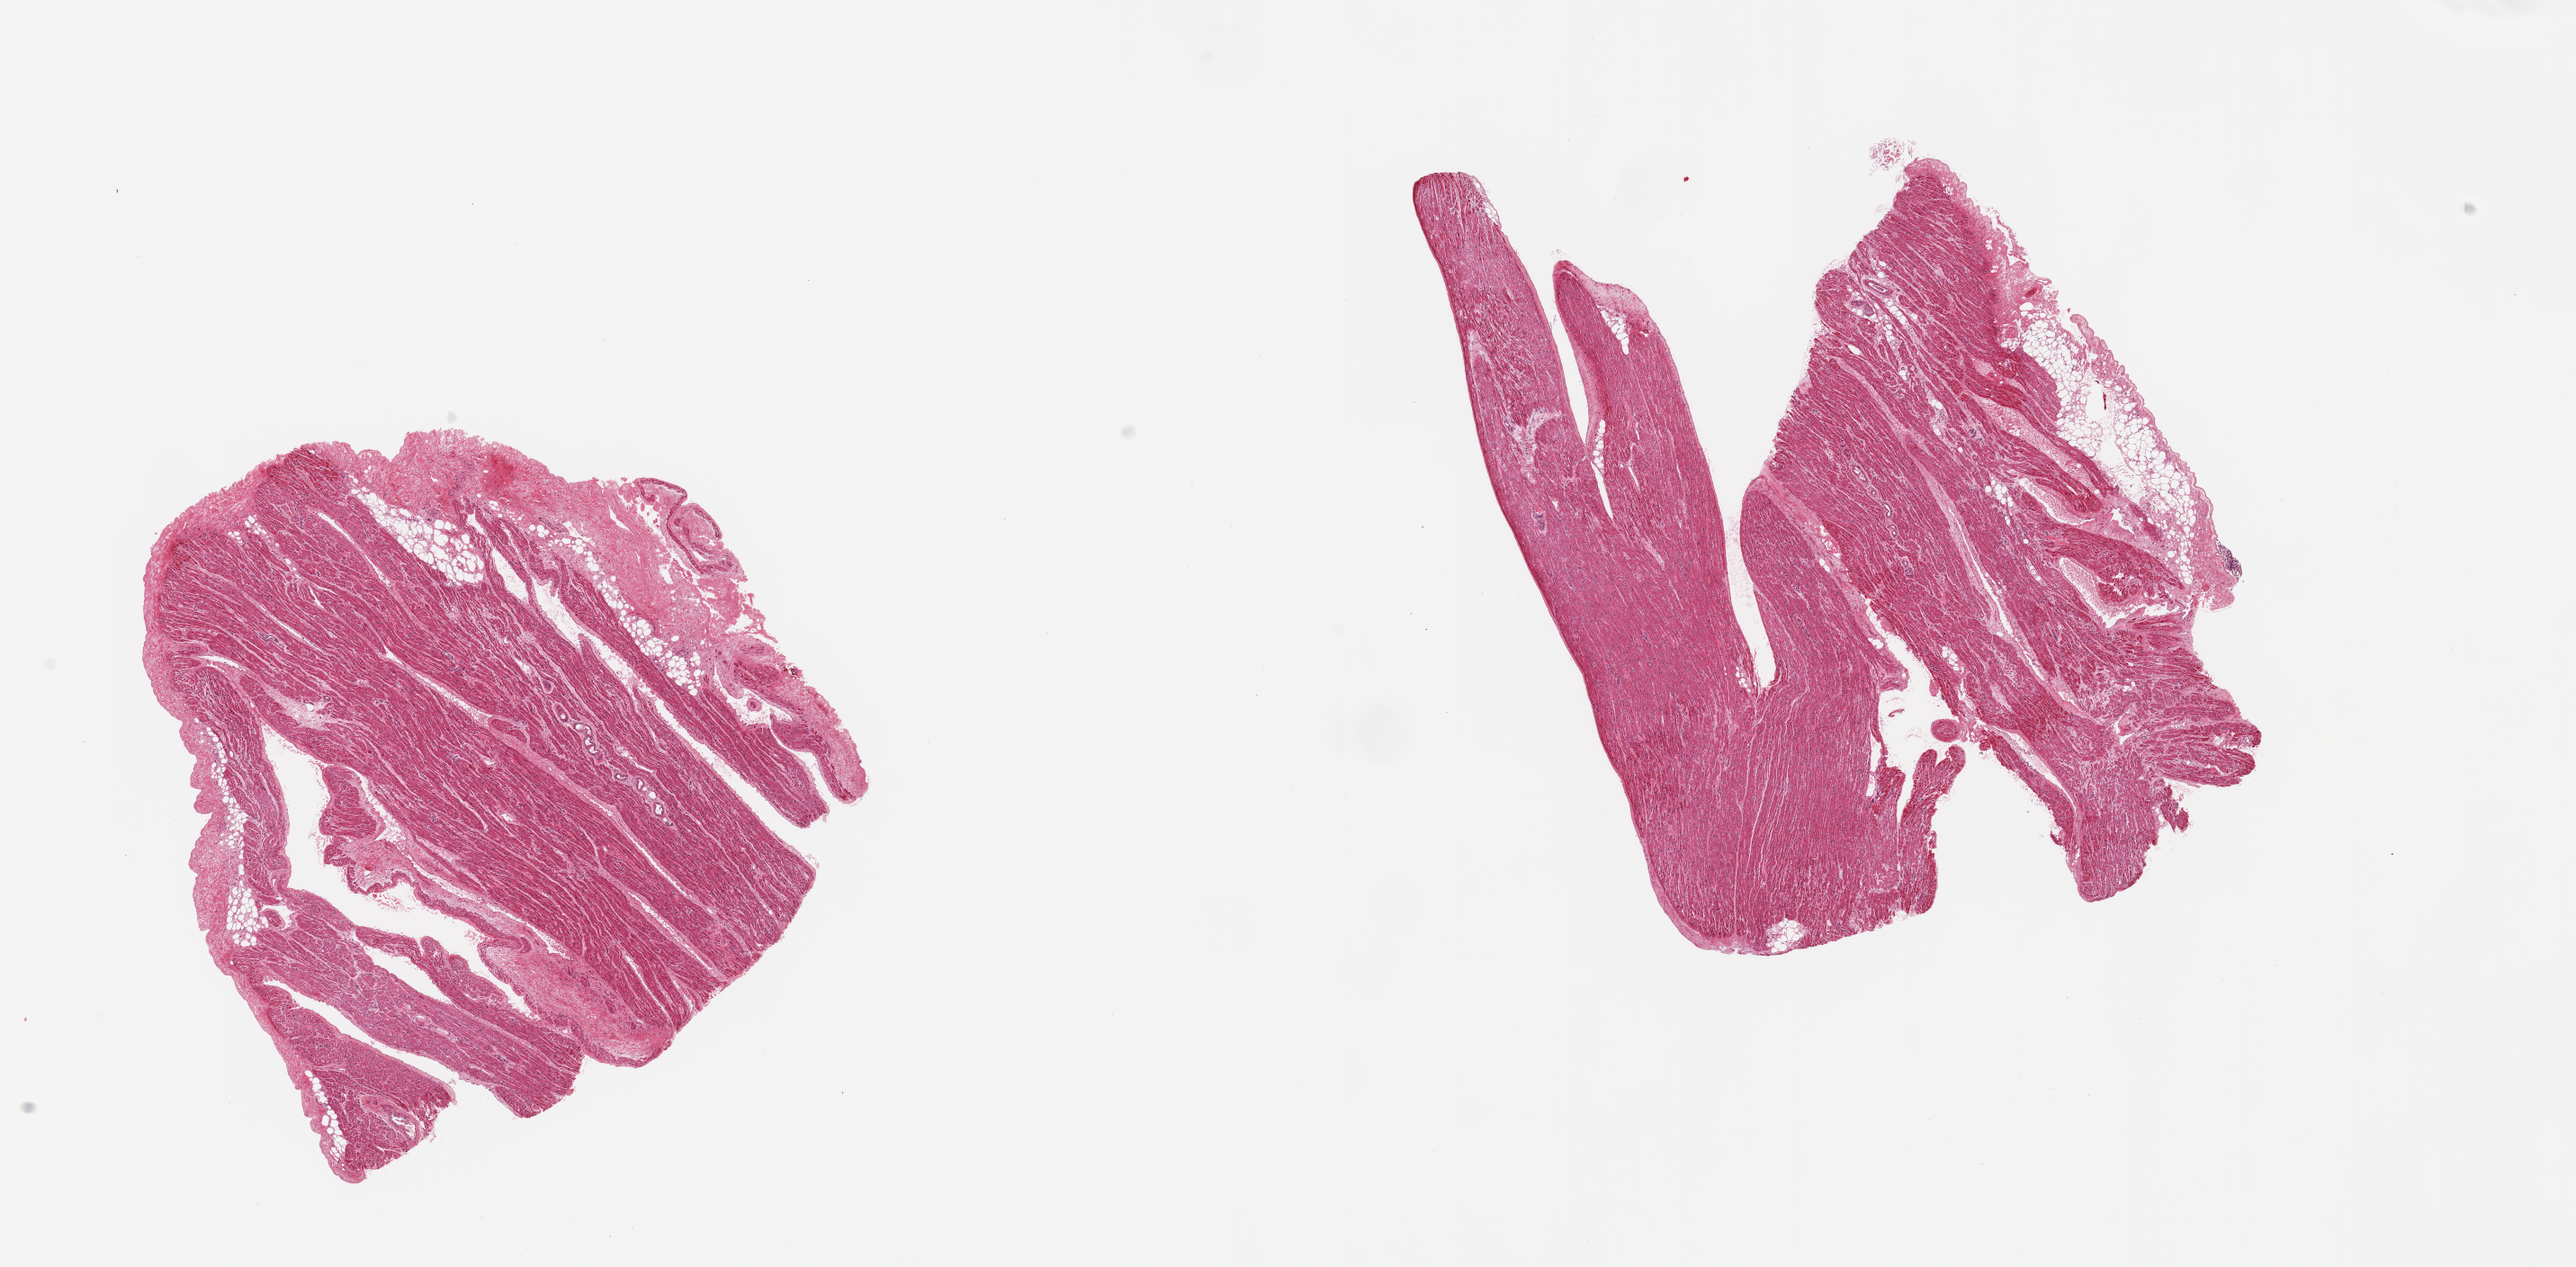
Haematoxylin and eosin whole-slide image, a low-resolution overview of the entire scanned area, about 22.6 x 11.1 mm (from a 20x scan). PAXgene-fixed, paraffin-embedded tissue. Sampled site (target tissue): auricular appendage. Donor tissue sample. Donor sex: female.
• reviewer comment on this tissue sample: 2 pieces; ~10% fibrous/fatty